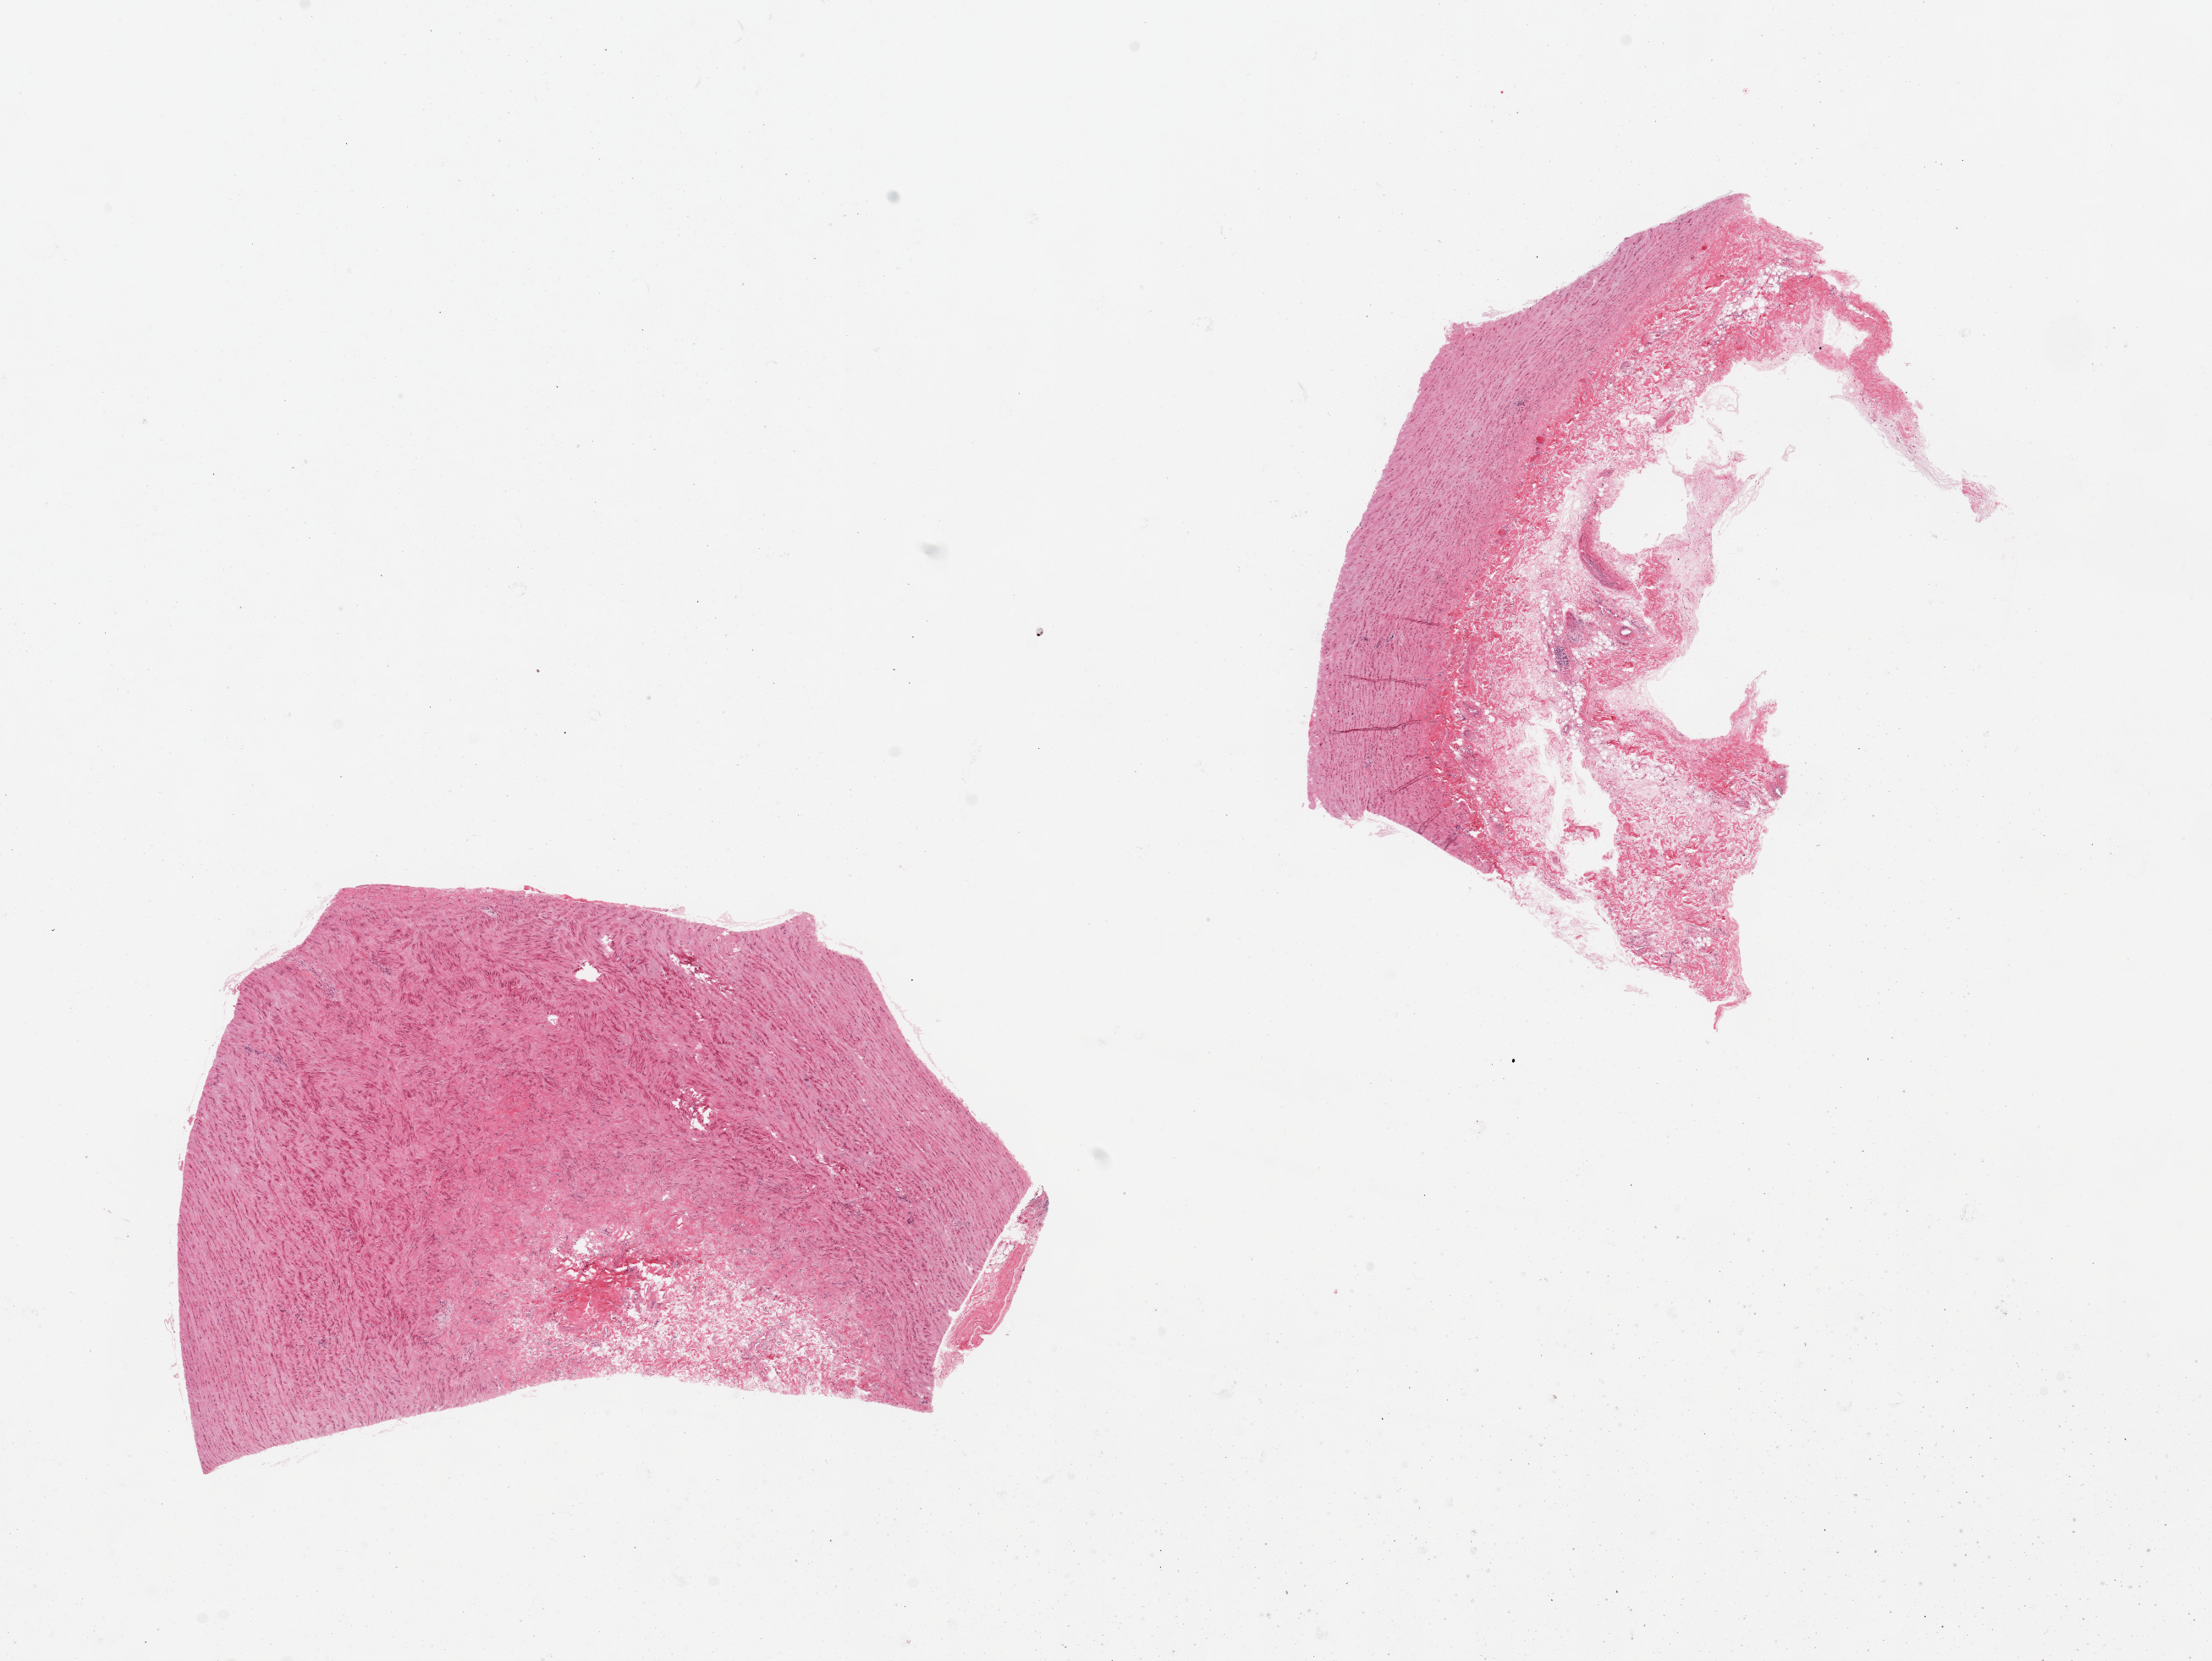
Digitized haematoxylin and eosin-stained section, whole scanned area (about 20.7 x 15.5 mm, slide scanned at 20x) shown as a low-resolution overview.
Specimen: PAXgene-fixed, paraffin-embedded tissue; sampled site (target tissue): auricular appendage; donor tissue sample.